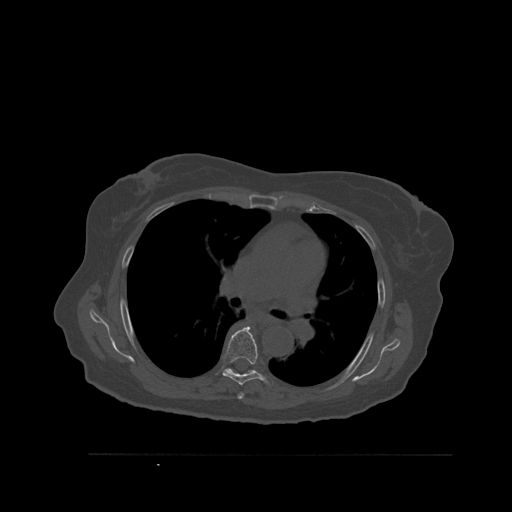
CT including the spine, one axial slice; slice 380 of 527 in the series (ordered by position); bone window (W 1800 / L 400 HU); 512 × 512 image matrix. Female patient, age 73 years. Case-level facts recorded for this patient, not image findings: primary cancer: breast.
Structures marked on this image (semi-automatic segmentation, software-assisted and operator-edited):
- T5 vertebra: bounding box [x1, y1, x2, y2] px = [237, 393, 244, 399]
- T6 vertebra: [222, 326, 274, 387]
- T7 vertebra: [246, 371, 249, 375]